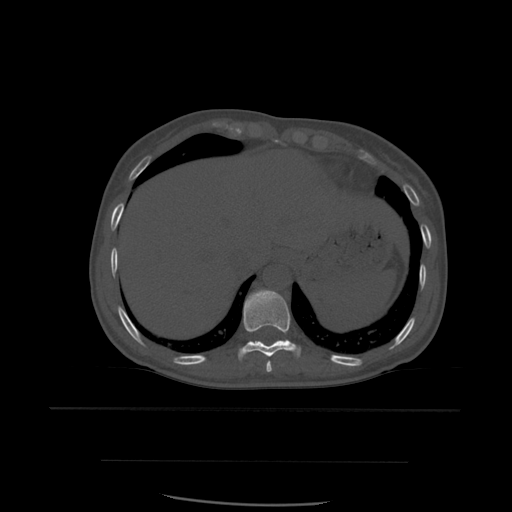
CT including the spine, one axial slice; bone window (W 1800 / L 400 HU); 1.25 mm slice thickness; 512 × 512 image matrix, field of view 392 × 392 mm. Patient age 48 years. From the clinical record (not read from this slice): primary cancer: lung.
Annotated regions visible in this slice (semi-automatically segmented with operator editing):
- T10 vertebra: bounding box [x1, y1, x2, y2] px = [238, 290, 302, 361]
- T11 vertebra: [258, 341, 266, 346]
- T9 vertebra: [266, 361, 273, 373]